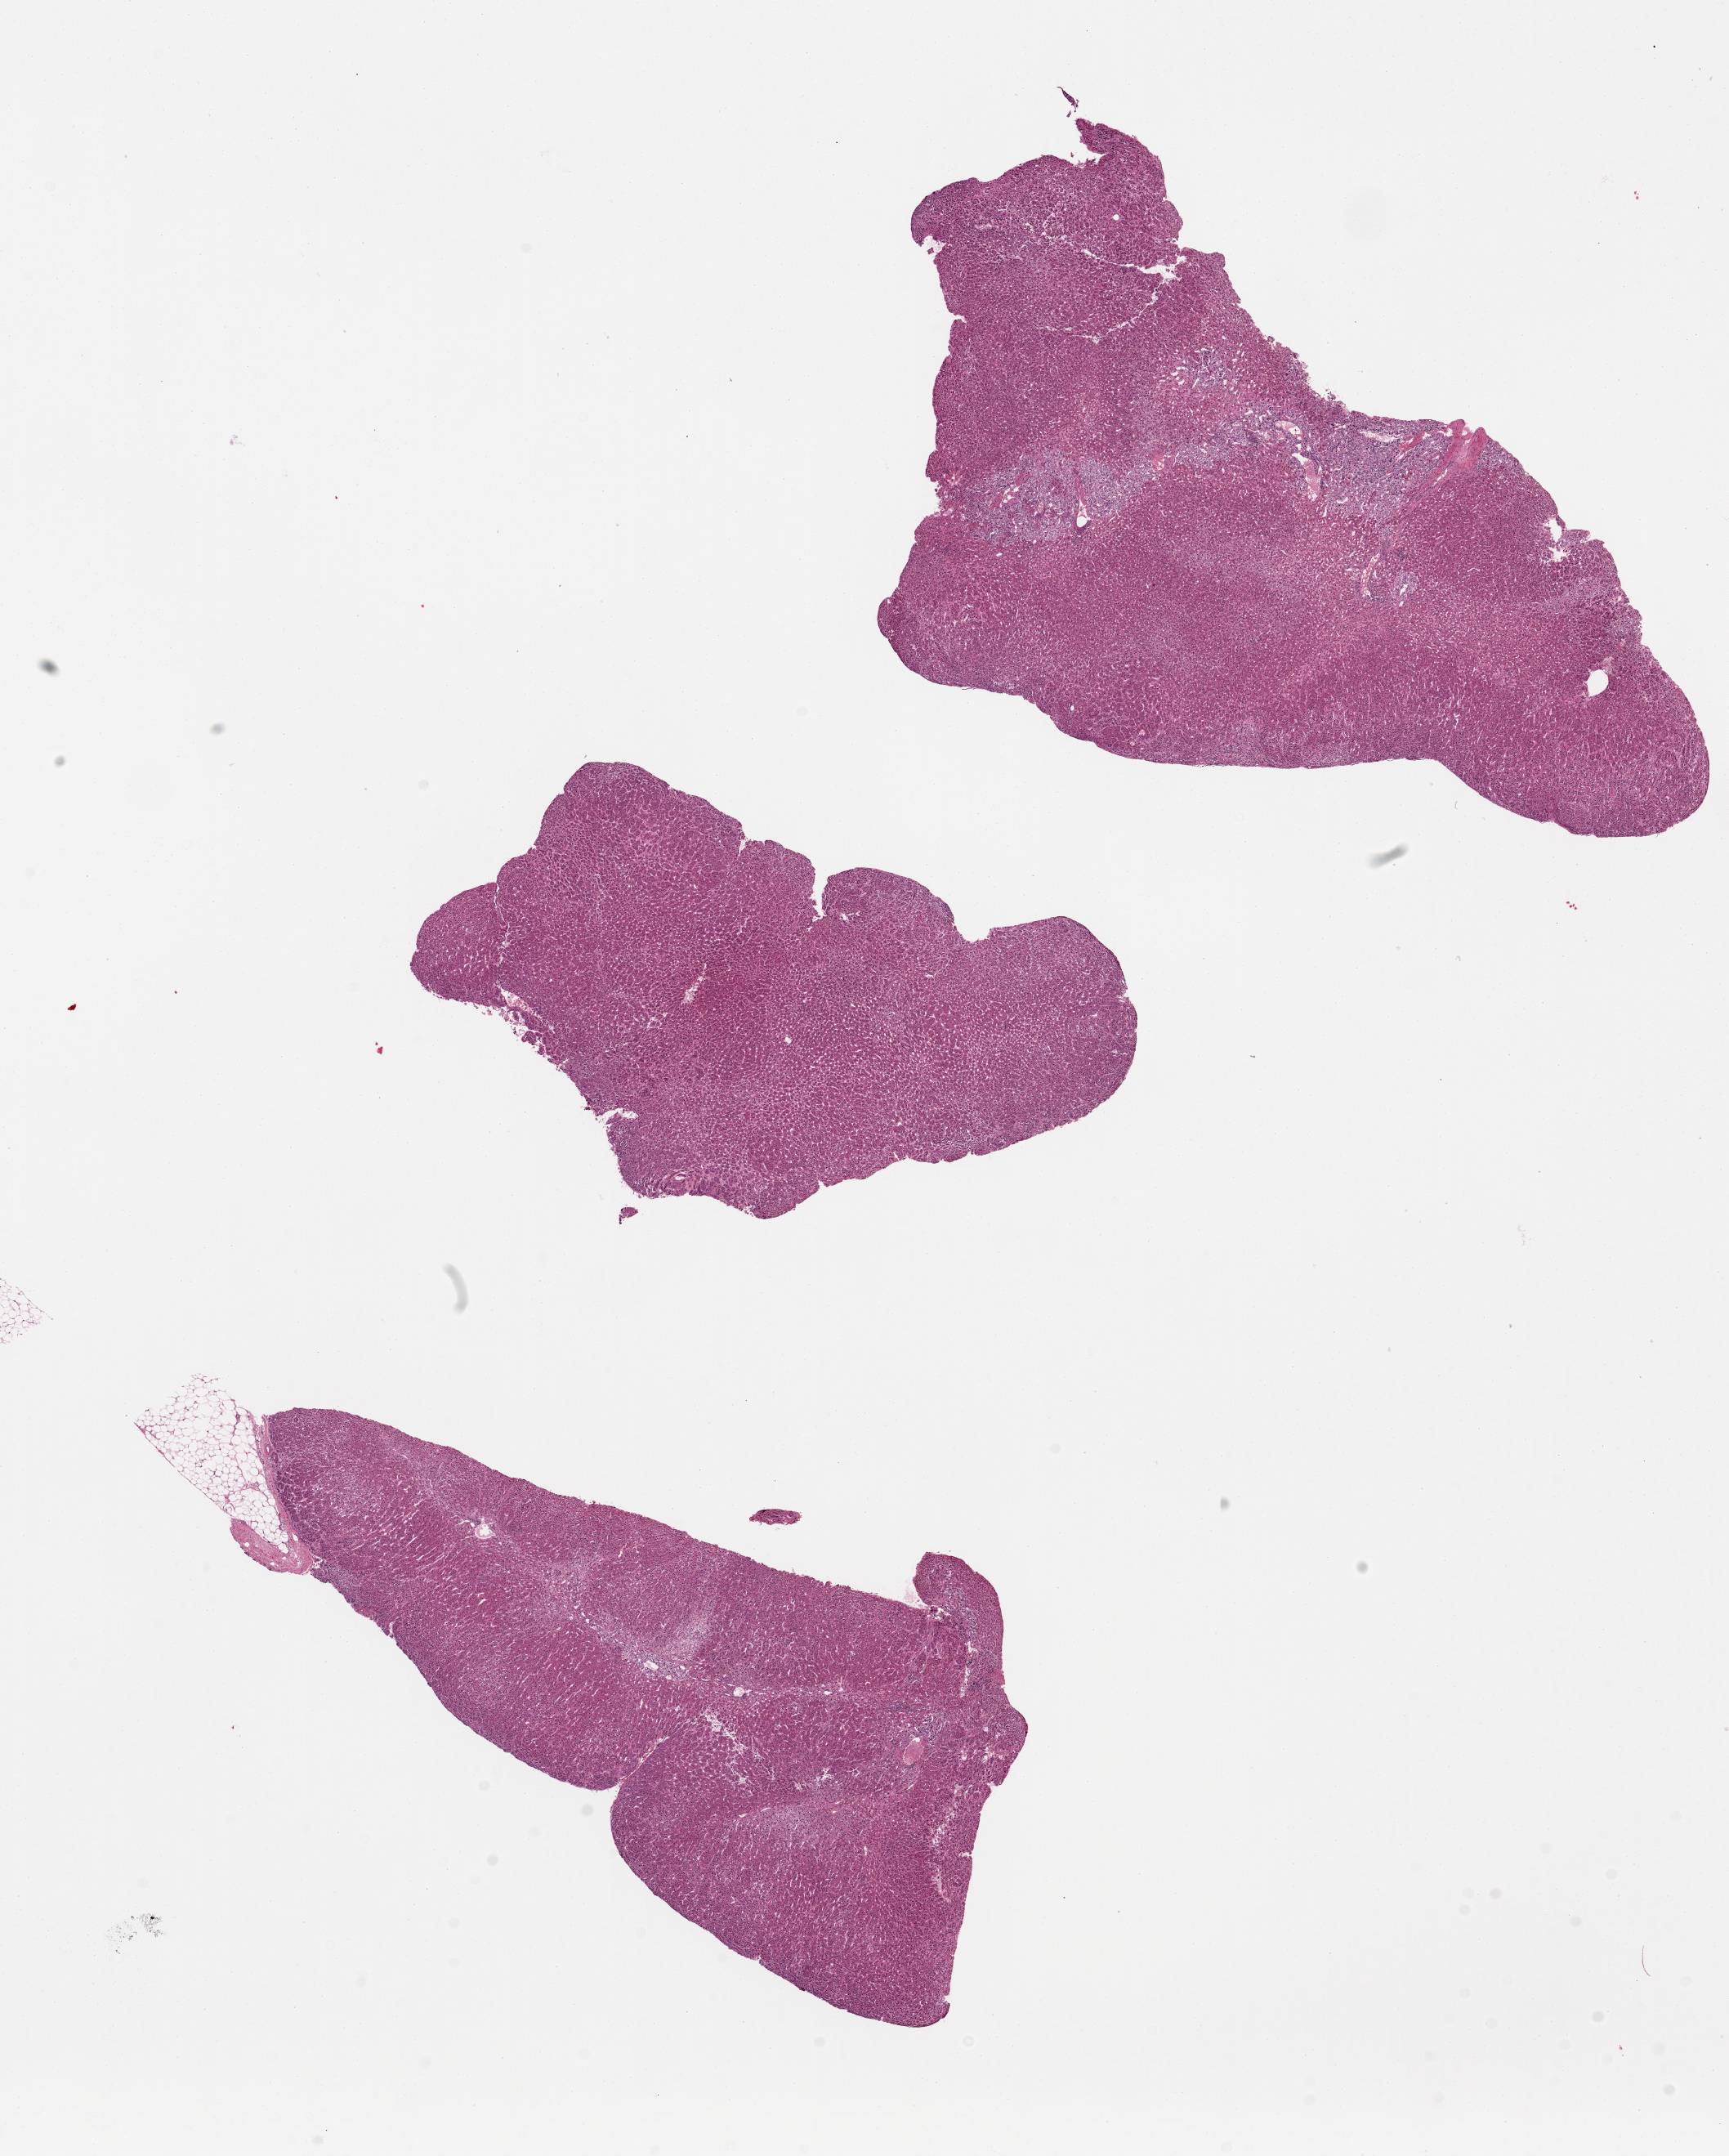
Digitized H&E-stained section, brightfield, low-resolution overview of the scanned area, about 16.7 x 20.9 mm; PAXgene-fixed, paraffin-embedded tissue; sampled site (target tissue): adrenal gland; donor tissue sample.
- review note (as recorded): 3 pieces, up to 10x6mm